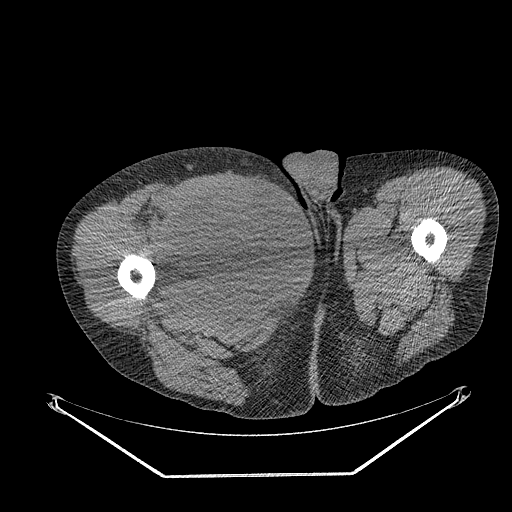
CT of an extremity soft-tissue mass (from a PET/CT study), one axial slice. Slice 275 of 311 in the series (ordered by position). Soft-tissue window (W 400 / L 40 HU). 3.75 mm slice thickness. 512 × 512 image matrix. Male patient. Case-level facts recorded for this patient, not image findings: histological type: undifferentiated - pleiomorphic; grade: high; site of the primary tumour: right thigh.
Annotated regions visible in this slice (expert contour drawn on MRI and transferred to this co-registered scan by the dataset authors):
- gross tumour volume including surrounding oedema: box from (x=164, y=178) to (x=266, y=280) px
- gross tumour volume (mass): (x=164, y=178)–(x=266, y=280)